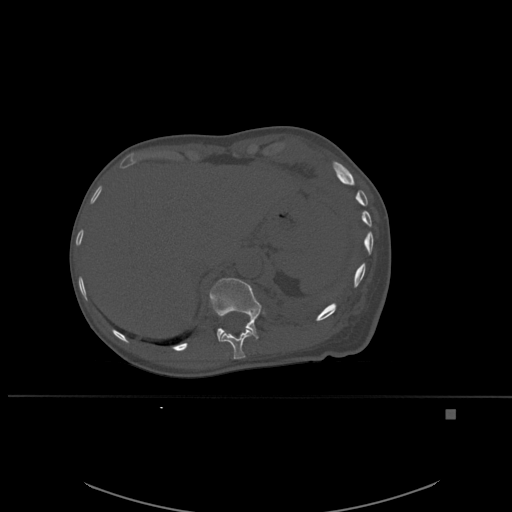
CT including the spine, one axial slice. Slice 290 of 537 in the series (ordered by position). Bone window (W 1800 / L 400 HU). 1.5 mm slice thickness. 512 × 512 image matrix. Female patient, age 45 years. From the clinical record (not read from this slice): primary cancer: lung.
Structures marked on this image (semi-automatically segmented with operator editing):
- T11 vertebra: bounding box [x1, y1, x2, y2] px = [210, 299, 254, 360]
- T12 vertebra: [209, 278, 263, 341]